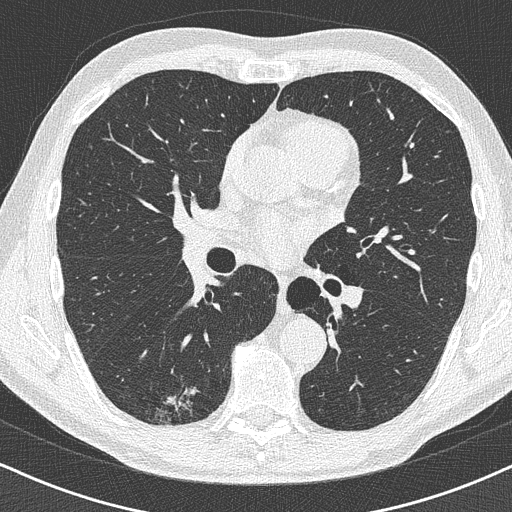
Chest CT (low-dose screening protocol), one axial image, baseline screening round, lung window (W 1500 / L -600 HU), 1 mm slice thickness, slice 203 of 438 in the series. Male participant, aged 63 years at enrolment. Former smoker at enrolment.
- Expert reader's lesion annotation, bounding box <141,377,212,431> (left, top, right, bottom; pixels).
- Reader record for this screening exam (exam-level; its link to the box is not recorded): non-calcified nodule or mass ≥4 mm, right lower lobe, 16 × 13 mm, poorly defined margins.
- Lung cancer was diagnosed 74 days after this screen: adenocarcinoma, NOS, right lower lobe, moderately differentiated (G2), stage IA (AJCC 6th edition), 20 mm at pathology.